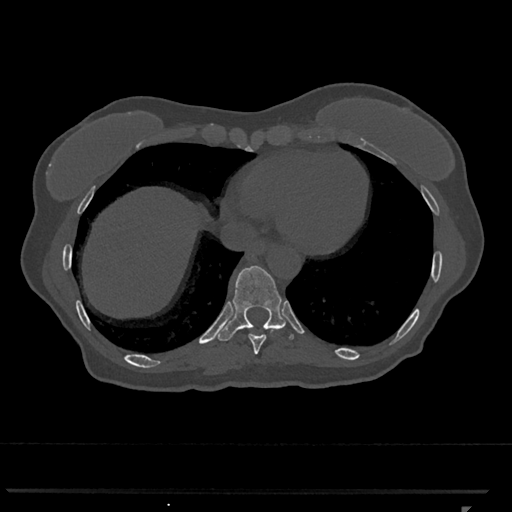
CT including the spine, one axial slice; reconstruction kernel Br40s/3; 120 kVp; bone window (W 1800 / L 400 HU); 0.5 mm slice thickness; 512 × 512 image matrix, field of view 380 × 380 mm. Female patient, age 62 years. From the clinical record (not read from this slice): primary cancer: renal.
Outlined on this slice (semi-automatic segmentation, software-assisted and operator-edited):
- T10 vertebra: bounding box [x1, y1, x2, y2] px = [217, 266, 294, 341]
- T9 vertebra: [249, 329, 274, 355]